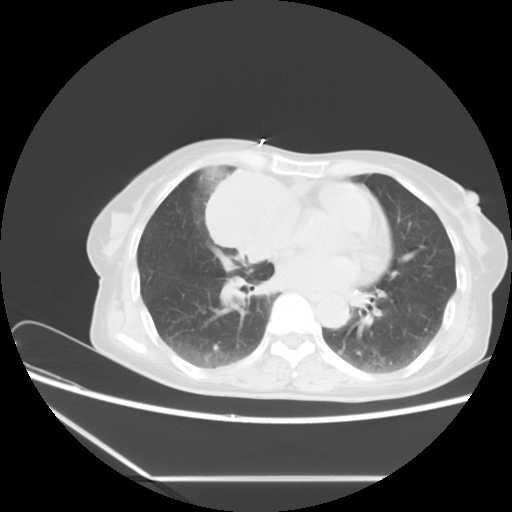
Chest CT, one axial slice. Position 3 of 16 along the scan axis. Lung window (W 1500 / L -600 HU). 512 × 512 image matrix. Female patient, age 63 years. From the clinical record (not read from this slice): clinical TNM (as recorded): T2b N1 M0.
Structures marked on this image (rectangle marked by the reading radiologist):
- lung tumour (recorded histology: adenocarcinoma): bounding box [x1, y1, x2, y2] px = [200, 165, 290, 265]